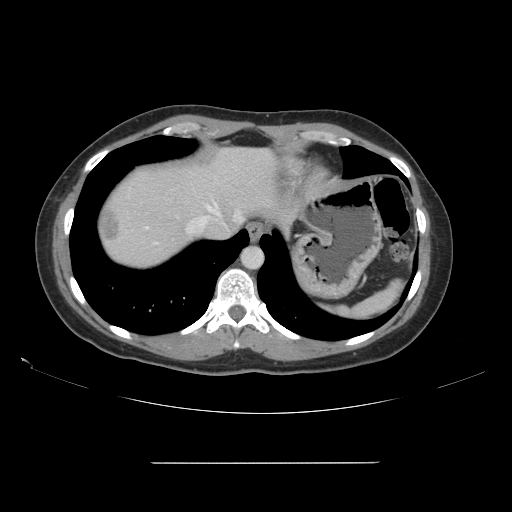
Contrast-enhanced abdominal CT, one axial slice. Intravenous contrast given. Soft-tissue window (W 400 / L 40 HU). 512 × 512 image matrix, field of view 421 × 421 mm. Female patient, age 46 years. From the clinical record (not read from this slice): diagnosis: colorectal cancer liver metastases, imaged before liver resection; multiple liver metastases: yes; largest metastasis: 3 cm.
Structures marked on this image (manually delineated by an expert):
- hepatic veins: bounding box <189,205,242,231> (left, top, right, bottom; pixels)
- liver: <97,148,275,268>
- planned liver remnant (the part of the liver to remain after resection): <111,149,276,234>
- liver metastasis: <101,206,121,245>